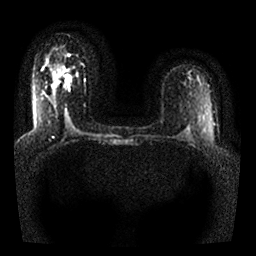
Breast MRI, one axial slice. Diffusion-weighted series; image 2 of 4 stored at this slice position (different b-values; order by instance number). 1.5 T. 256 × 256 image matrix, field of view 330 × 330 mm. Female patient.
Annotated regions visible in this slice (outlined manually by an expert reader):
- tumour on diffusion-weighted imaging: bounding box [x1, y1, x2, y2] px = [66, 76, 70, 84]